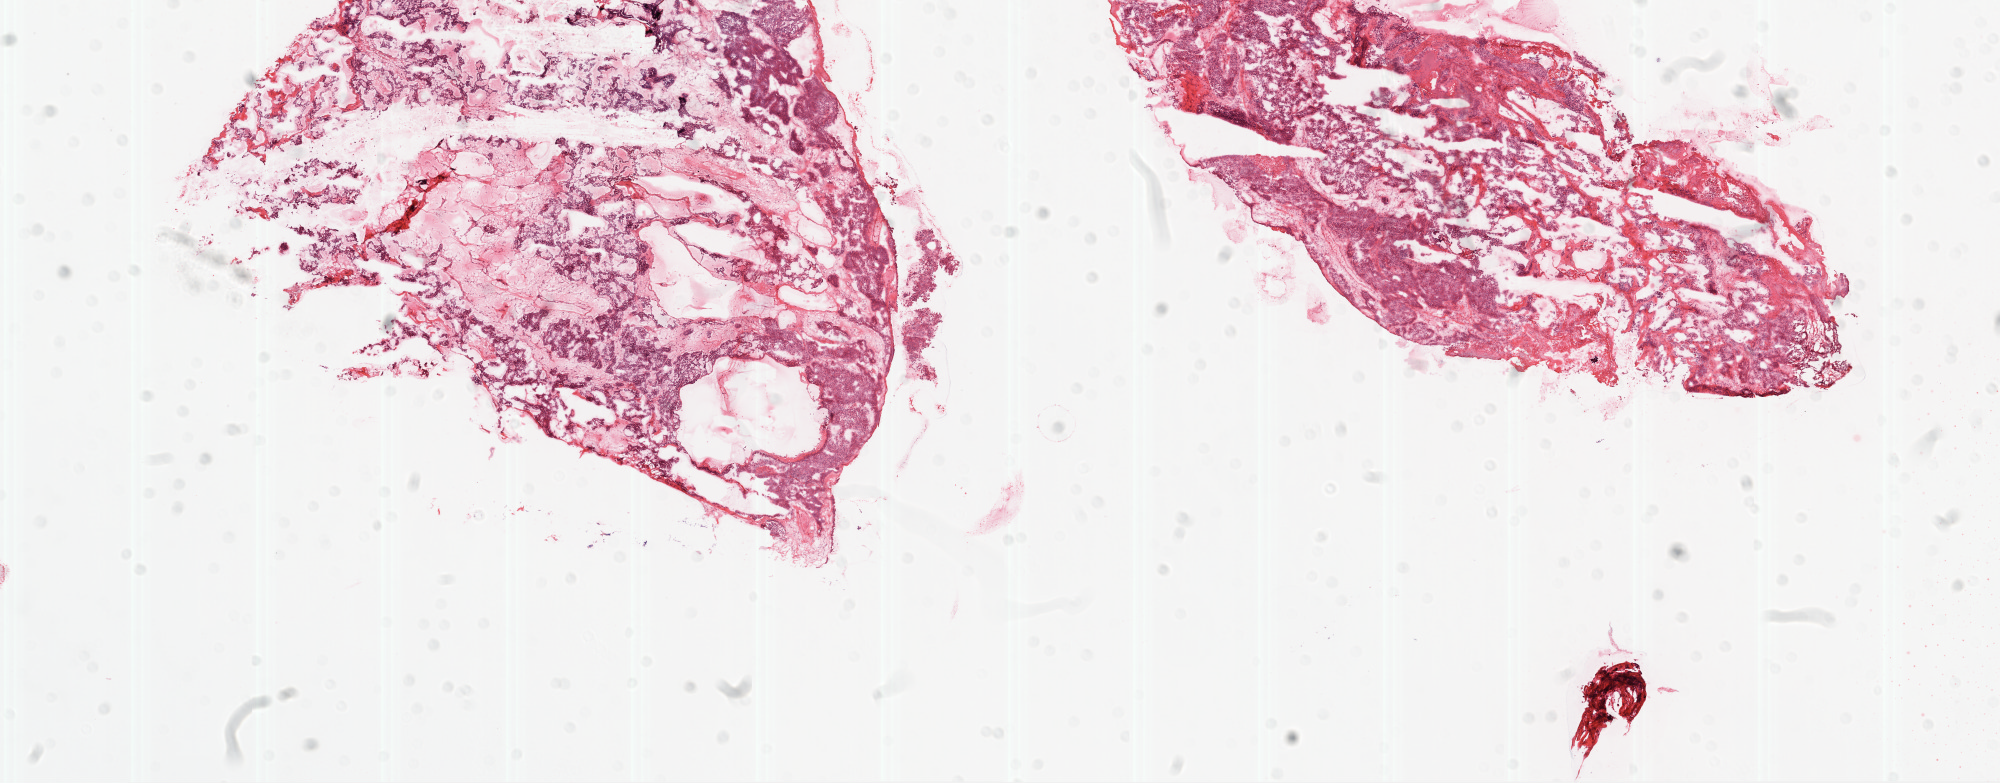
Whole-slide histology image, H&E, a low-resolution overview of the entire scanned area, about 16.0 x 6.3 mm (slide scanned at 20x), frozen section from the top of the tissue portion, sample: primary tumour, ovary. Patient: female, age at initial diagnosis 56 years.
Histologic diagnosis: Serous cystadenocarcinoma, NOS.